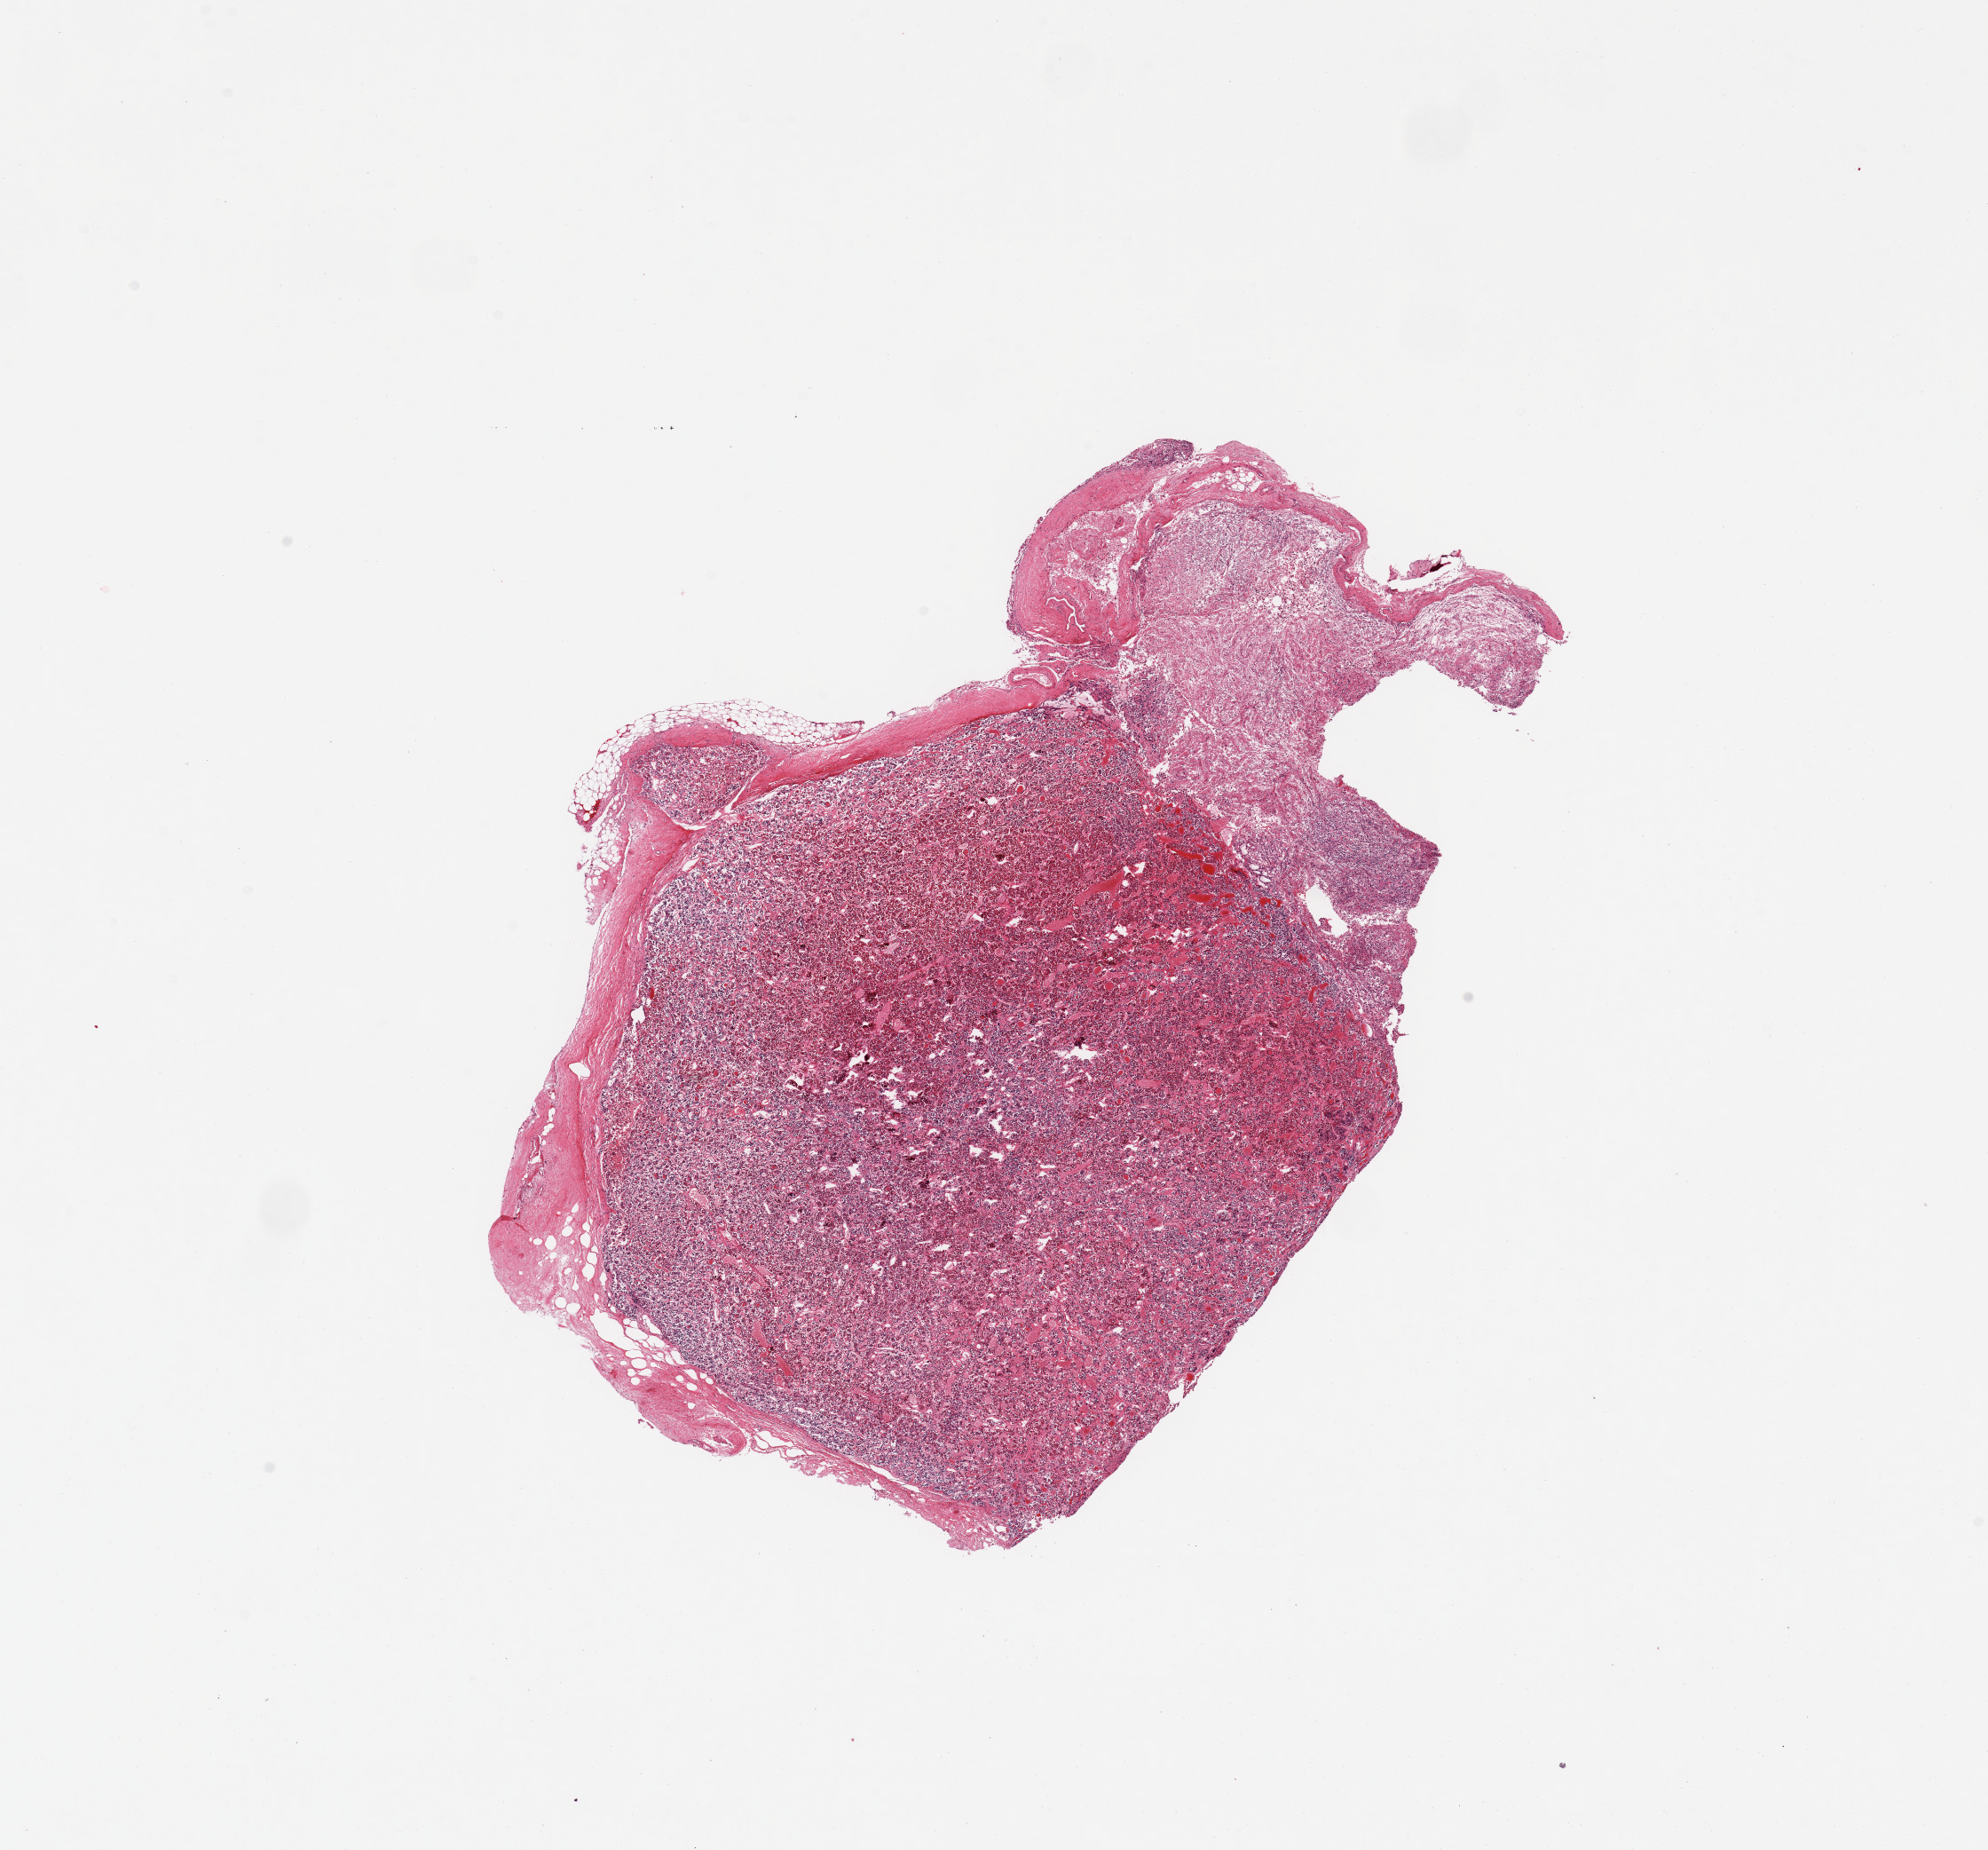
Digitized hematoxylin and eosin (H&E)-stained section — a low-resolution overview of the entire scanned area, about 17.7 x 16.5 mm (from a 20x scan); PAXgene-fixed paraffin-embedded (PFPE) section; sampled site (target tissue): pituitary; donor tissue sample. Donor sex: female.
Review note (as recorded): 1 piece, mainly adenohypophysis; ~3x3mm focus of neurohypophysis.